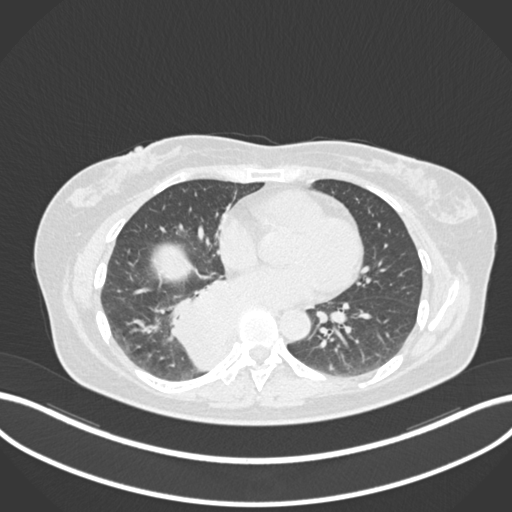
Chest CT, one axial slice. Slice 569 of 677 in the series (ordered by position). Reconstruction kernel B30f. Lung window (W 1500 / L -600 HU). 1 mm slice thickness. 512 × 512 image matrix, field of view 400 × 400 mm. Female patient, age 54 years. From the clinical record (not read from this slice): clinical TNM (as recorded): T4 N0 M0.
Outlined on this slice (bounding box drawn by a radiologist):
- lung tumour (recorded histology: adenocarcinoma): bounding box <163,272,244,374> (left, top, right, bottom; pixels)